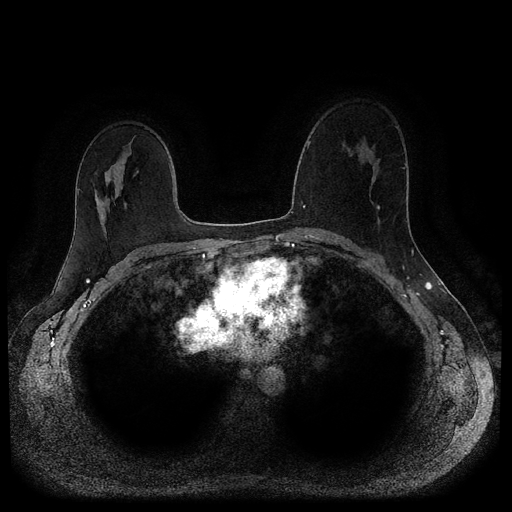
Breast MRI (dynamic contrast-enhanced, multi-phase), one axial slice. Slice 64 of 116 in the series (ordered by position). Dynamic contrast-enhanced series, time point 2 of 5 at this slice position (early post-contrast). 1.5 T. TE 2.6 ms, TR 5.3 ms. 2 mm slice thickness. 512 × 512 image matrix, field of view 350 × 350 mm. Female patient, age 45 years.
Structures marked on this image (semi-automatic segmentation, software-assisted and operator-edited):
- breast lesion (labelled 'tumour' in the annotation; benign lesions carry a separate 'benign' label): box from (x=376, y=205) to (x=380, y=210) px